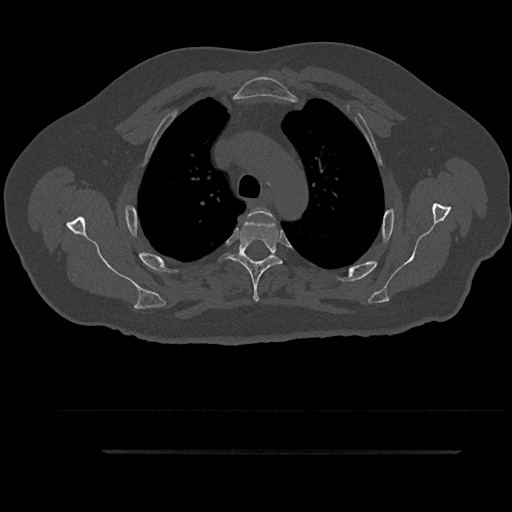
CT including the spine, one axial slice; position 675 of 797 along the scan axis; reconstruction kernel Br40s/3; 120 kVp; bone window (W 1800 / L 400 HU); 0.5 mm slice thickness; 512 × 512 image matrix, field of view 432 × 432 mm. Male patient, age 63 years. Case-level facts recorded for this patient, not image findings: primary cancer: renal; vertebrae with lytic lesions (as recorded): T8.
Structures marked on this image (semi-automatically segmented with operator editing):
- T3 vertebra: bounding box [x1, y1, x2, y2] px = [248, 207, 272, 261]
- T4 vertebra: [217, 216, 282, 302]